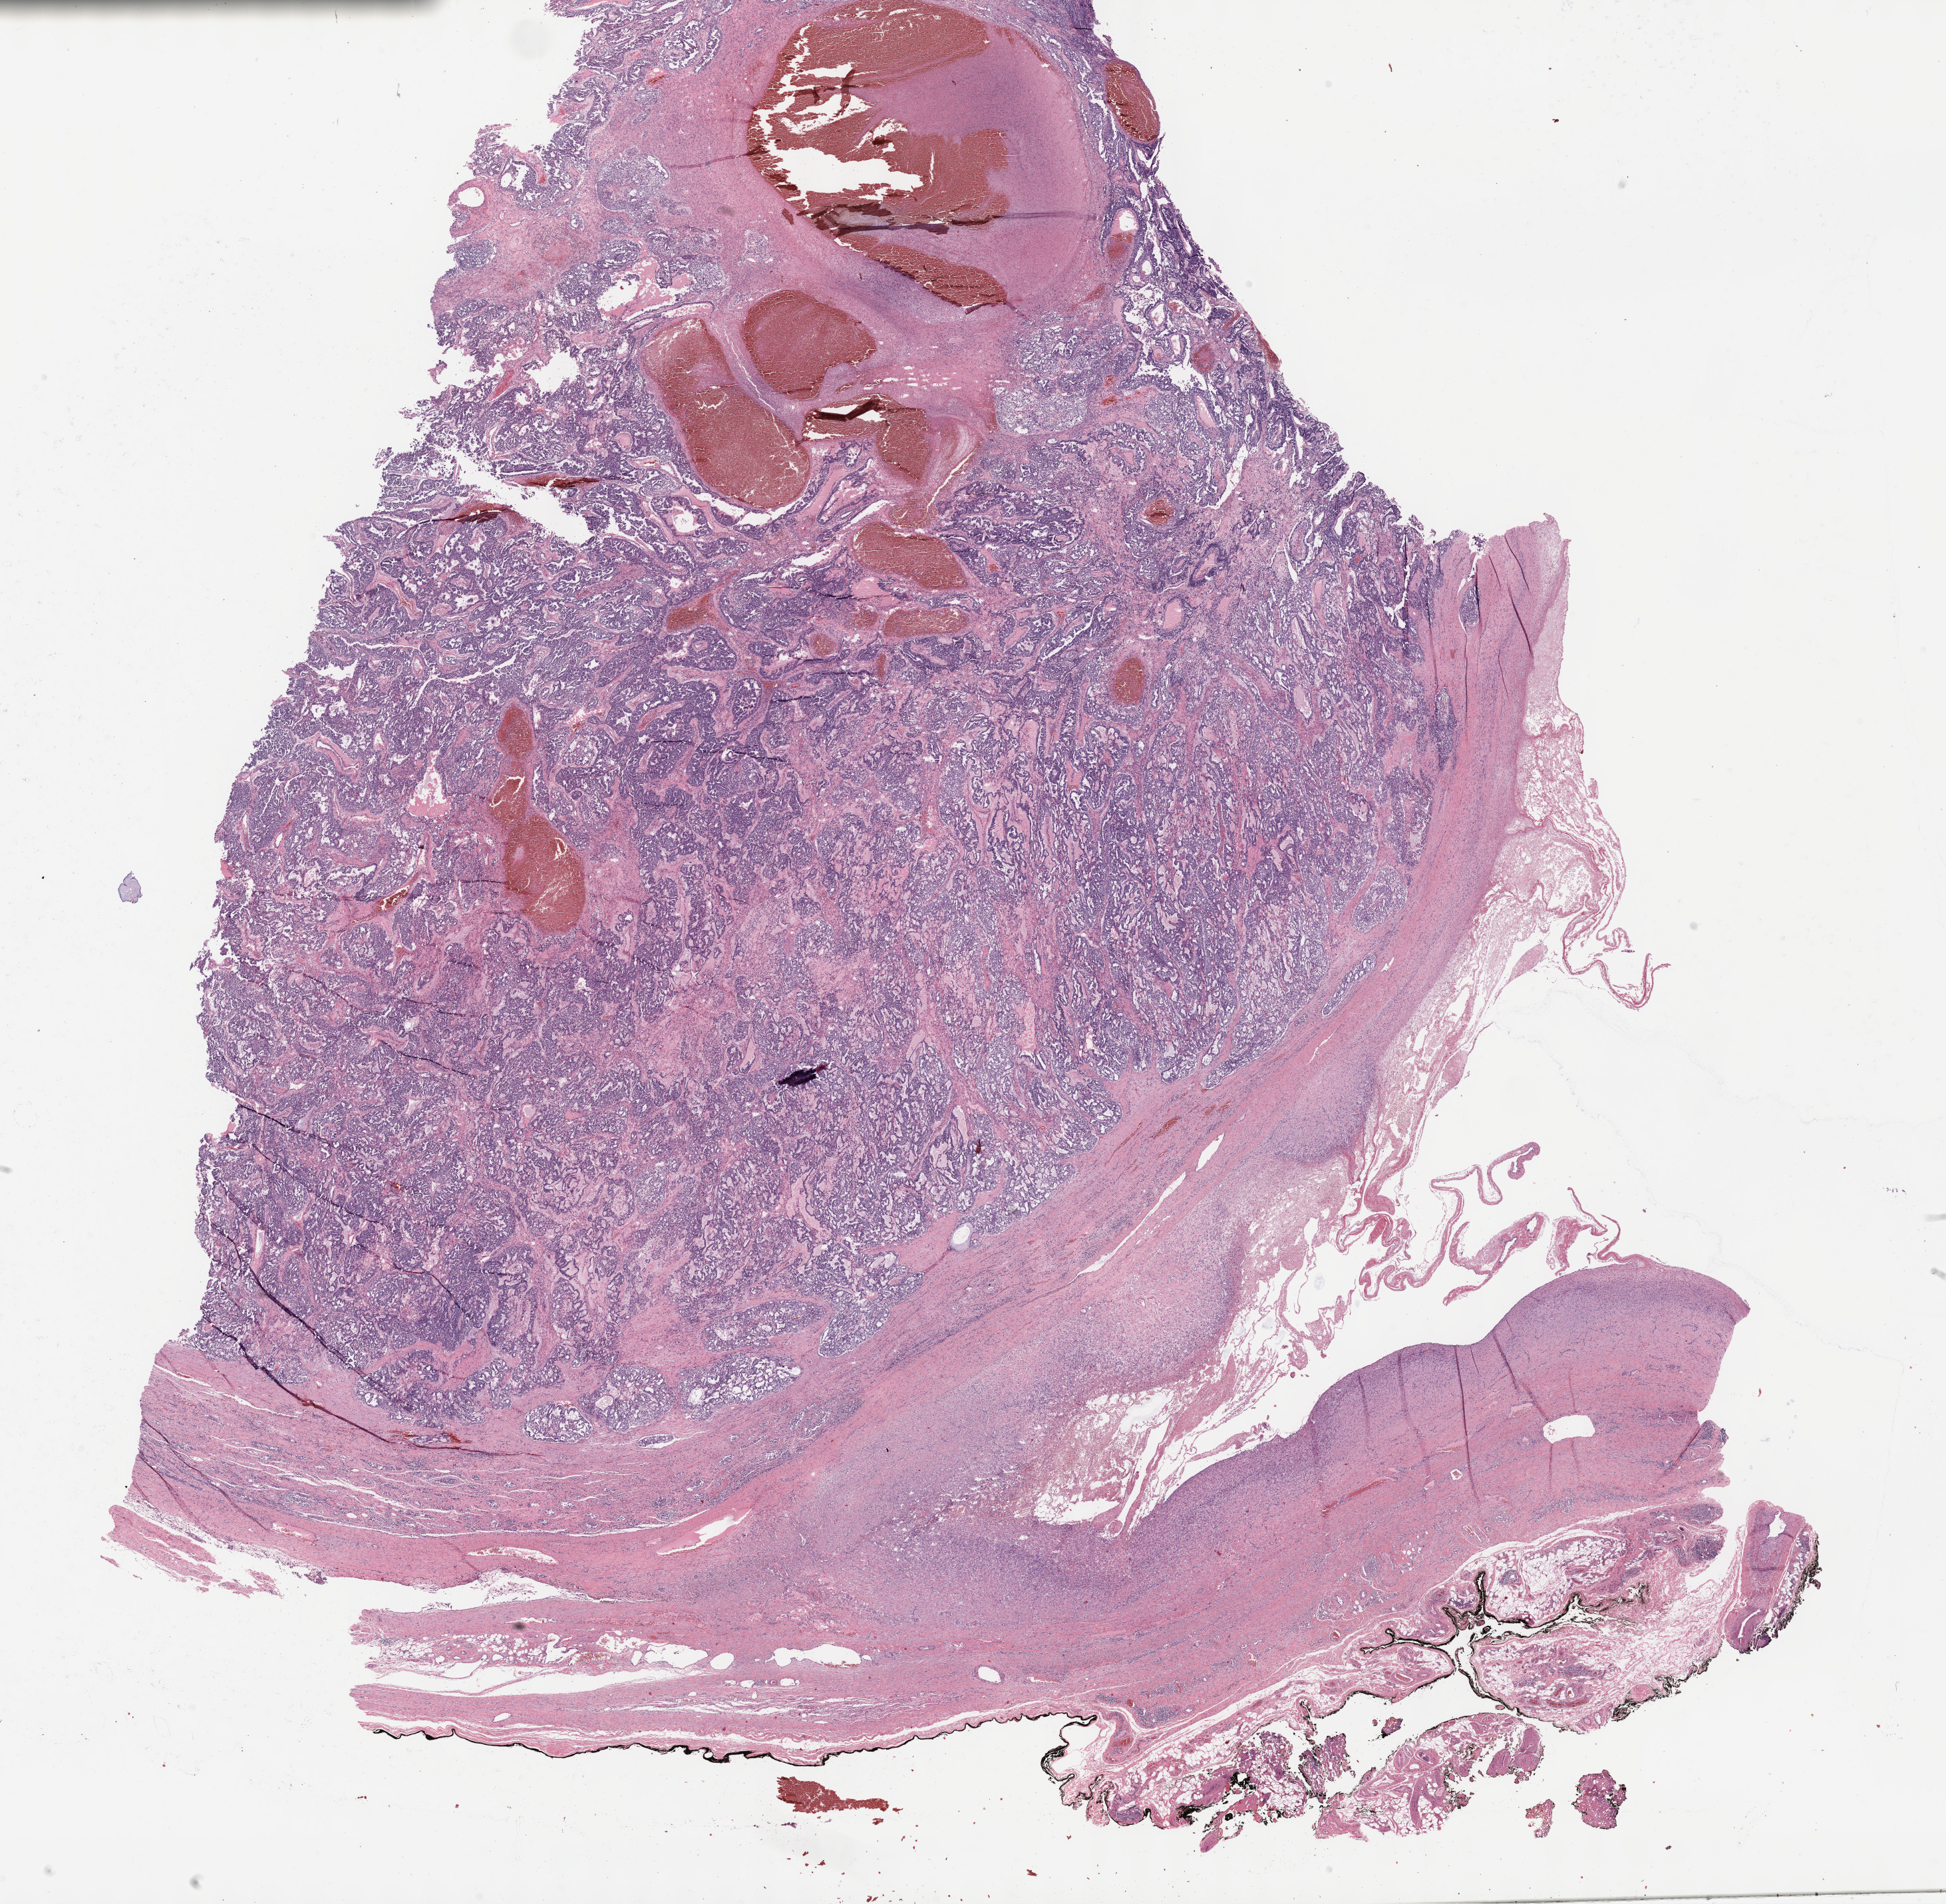
Hematoxylin and eosin (H&E) stained whole-slide image — low-resolution overview of the scanned area, about 23.7 x 23.1 mm; FFPE section; primary tumour sample from the testis. Male, age 66 years at initial diagnosis.
Diagnosis: Yolk sac tumor.